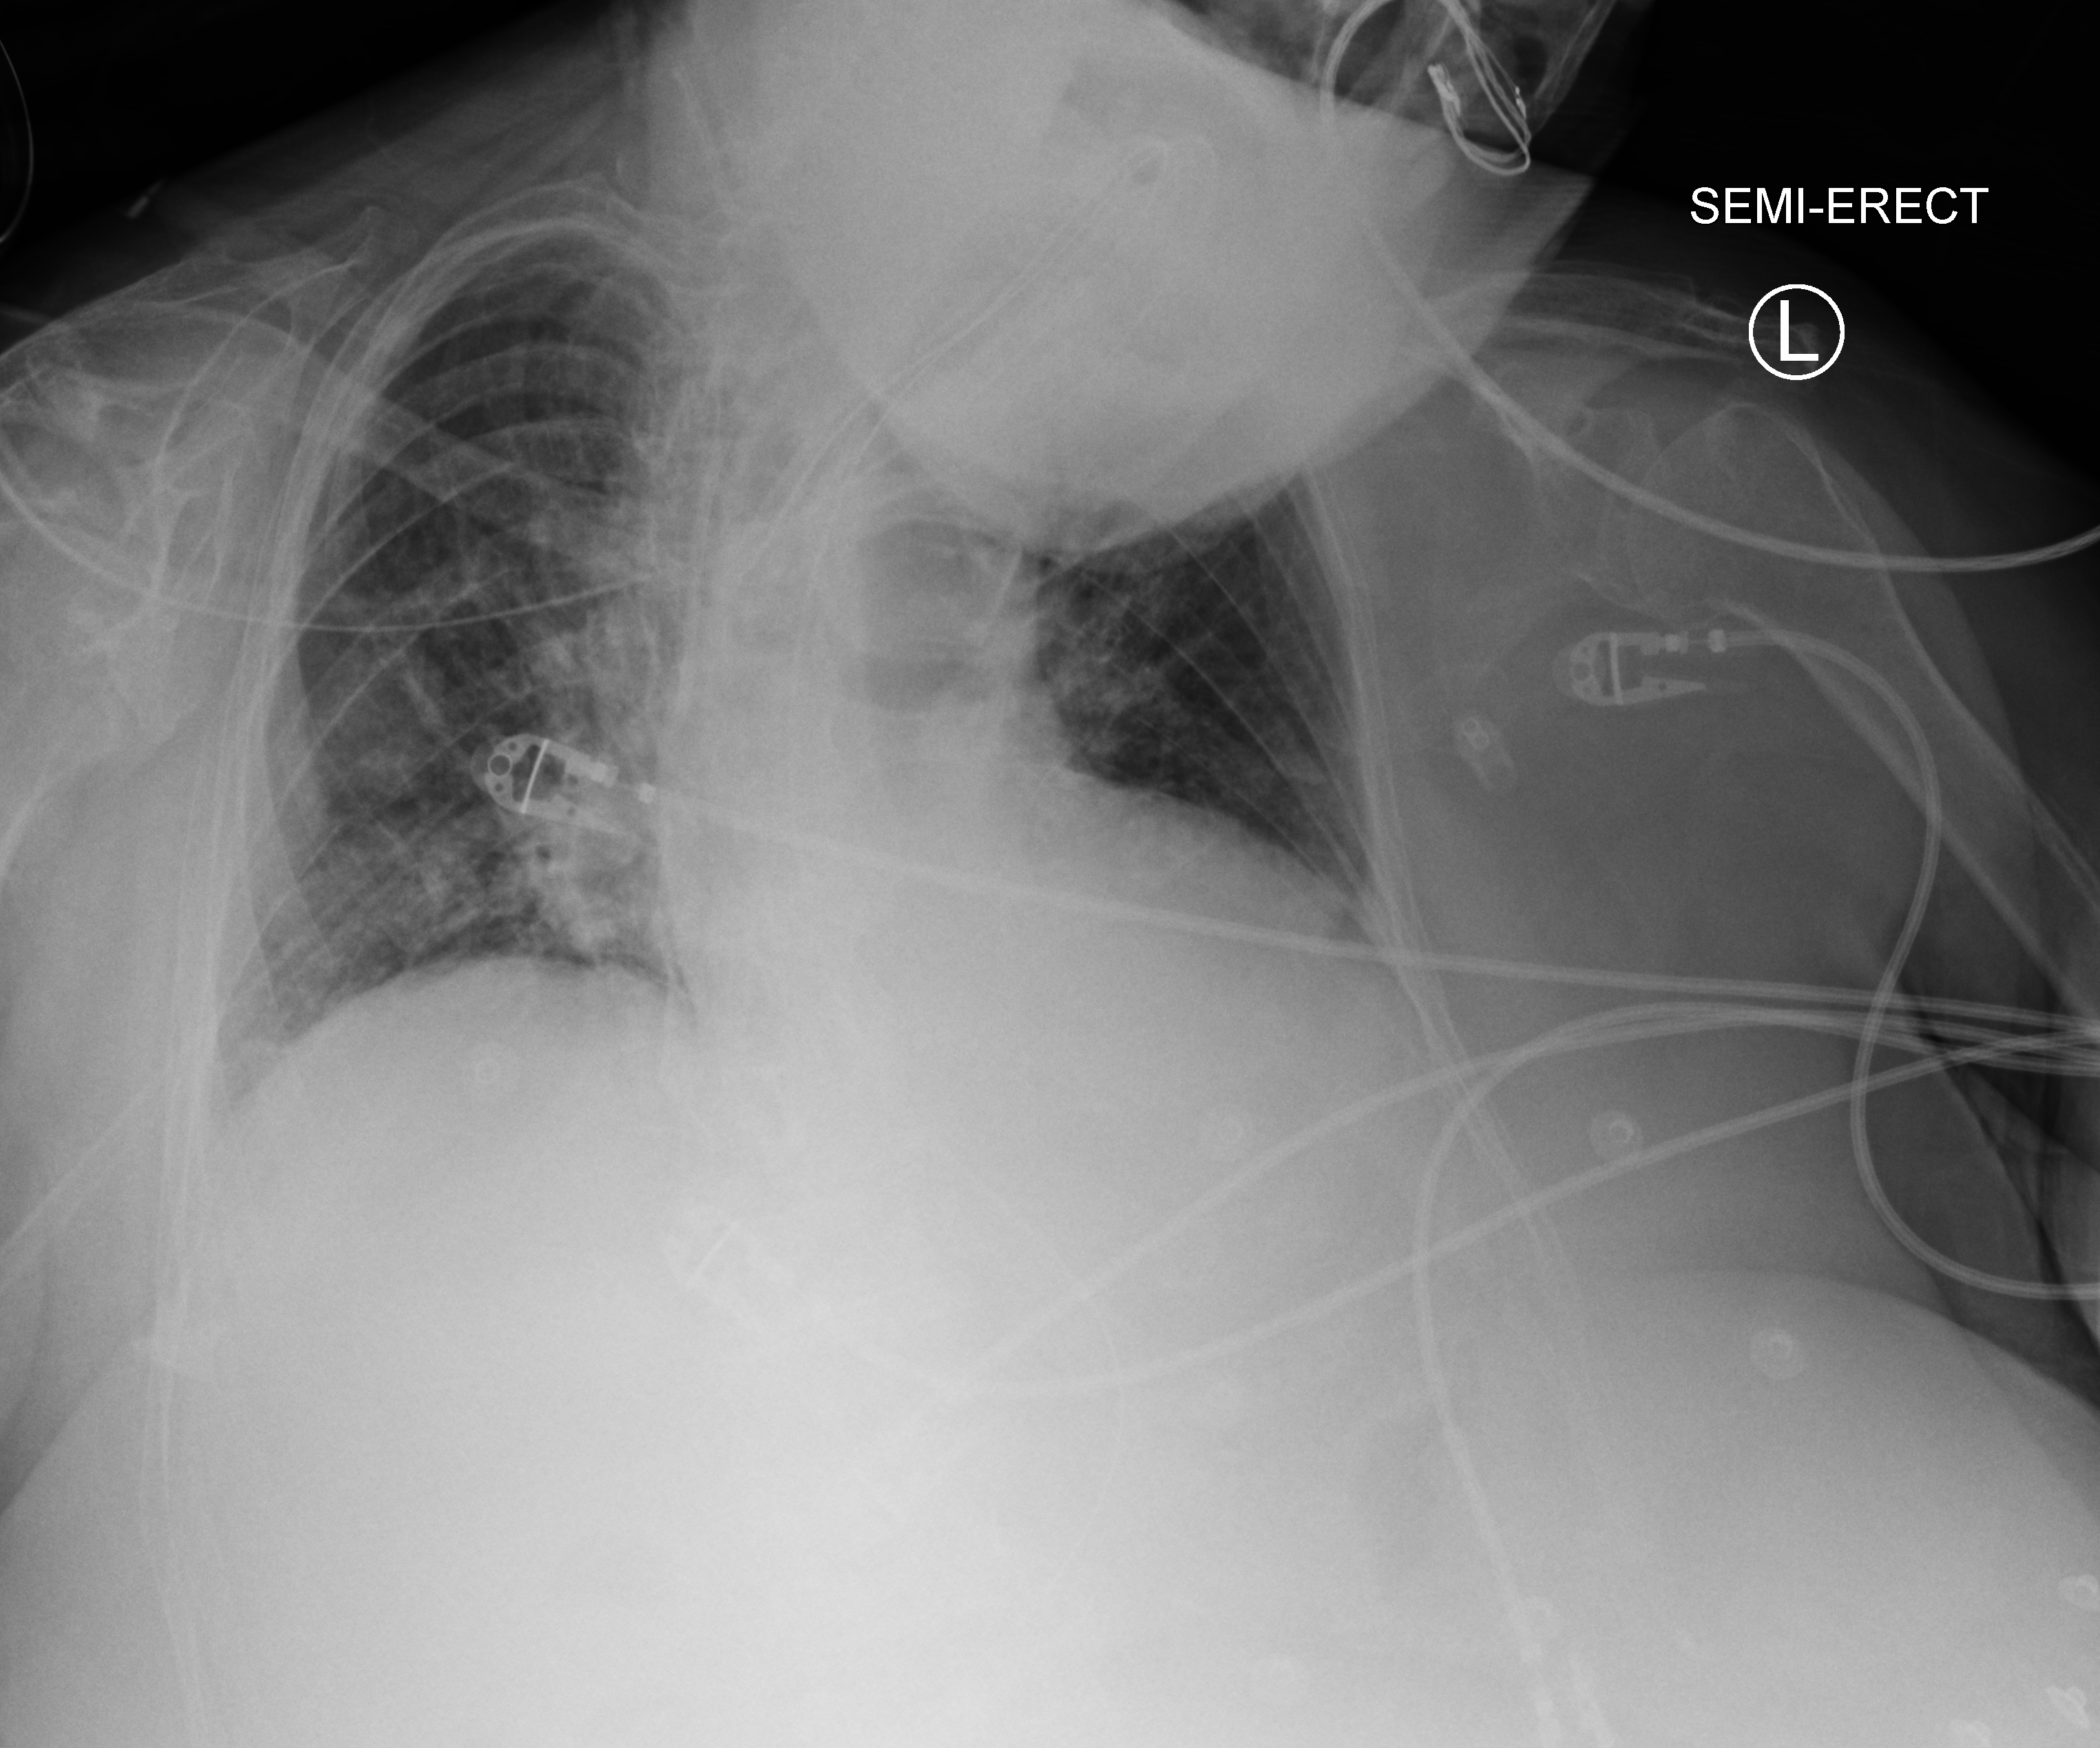
Bedside chest radiograph (computed radiography); anteroposterior (AP) projection. Patient hospitalised with COVID-19; female, aged 75–90 years.
Admission-level facts for this patient (not findings on this image; timing relative to this image not recorded):
- COPD (admission record): yes